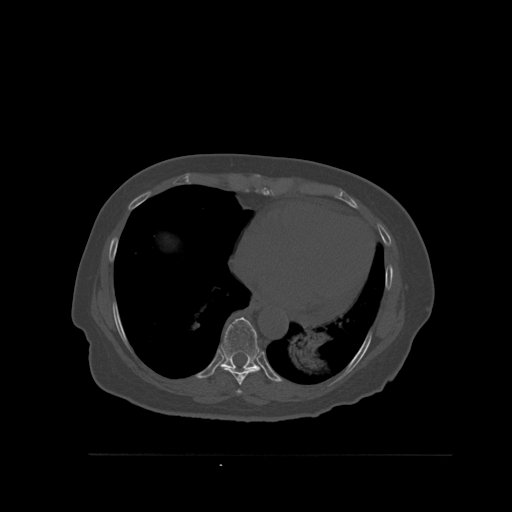
CT including the spine, one axial slice; bone window (W 1800 / L 400 HU); 1.5 mm slice thickness; 512 × 512 image matrix, field of view 470 × 470 mm. Female patient, age 73 years. Case-level facts recorded for this patient, not image findings: primary cancer: breast; vertebrae with lytic lesions (as recorded): L2.
Structures marked on this image (semi-automatic segmentation, software-assisted and operator-edited):
- T7 vertebra: box from (x=237, y=389) to (x=242, y=394) px
- T8 vertebra: (x=223, y=366)–(x=261, y=385)
- T9 vertebra: (x=219, y=317)–(x=259, y=372)